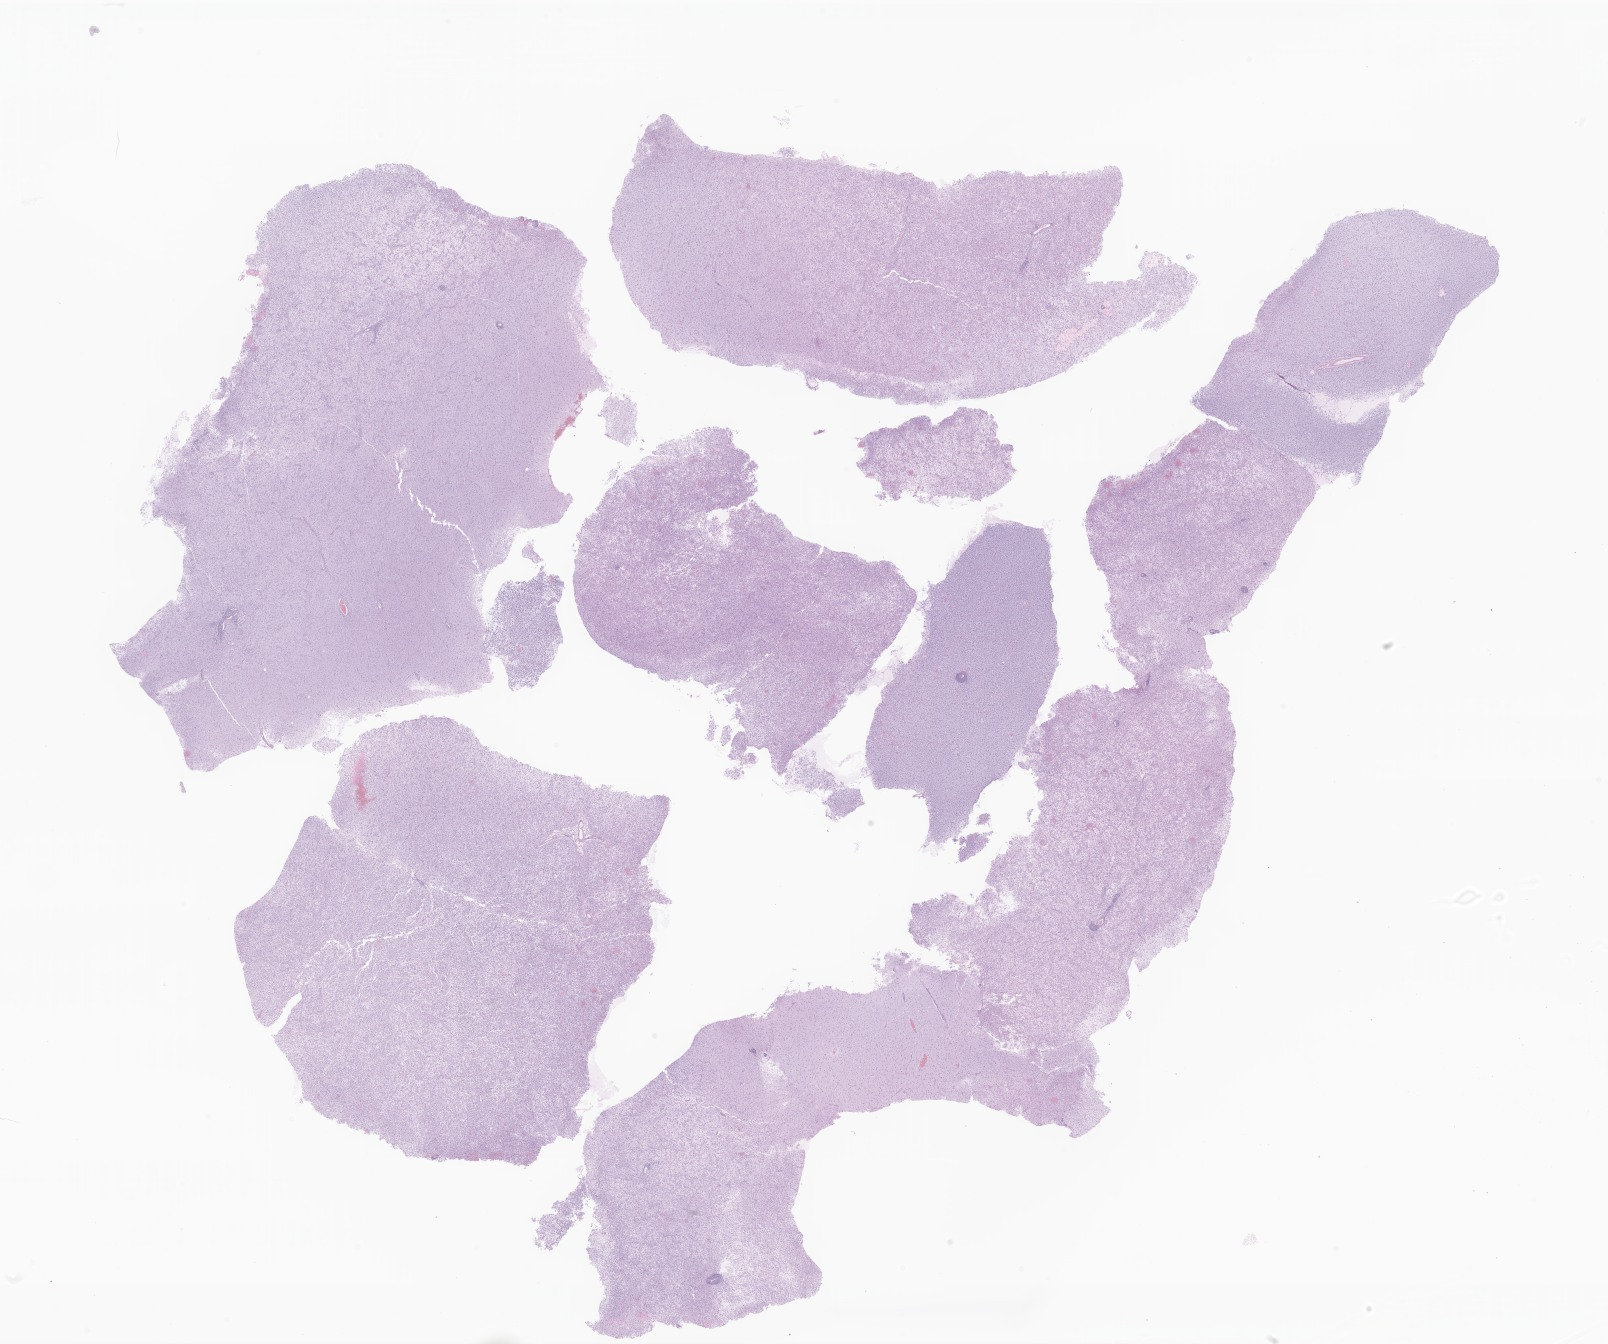
Hematoxylin and eosin (H&E) whole-slide image of tumor tissue from the brain, low-resolution overview of the scanned area, about 27.1 x 22.7 mm; FFPE section. Patient: male, age 159 months (13 years 3 months).
Recorded diagnosis: Neoplasm, malignant.